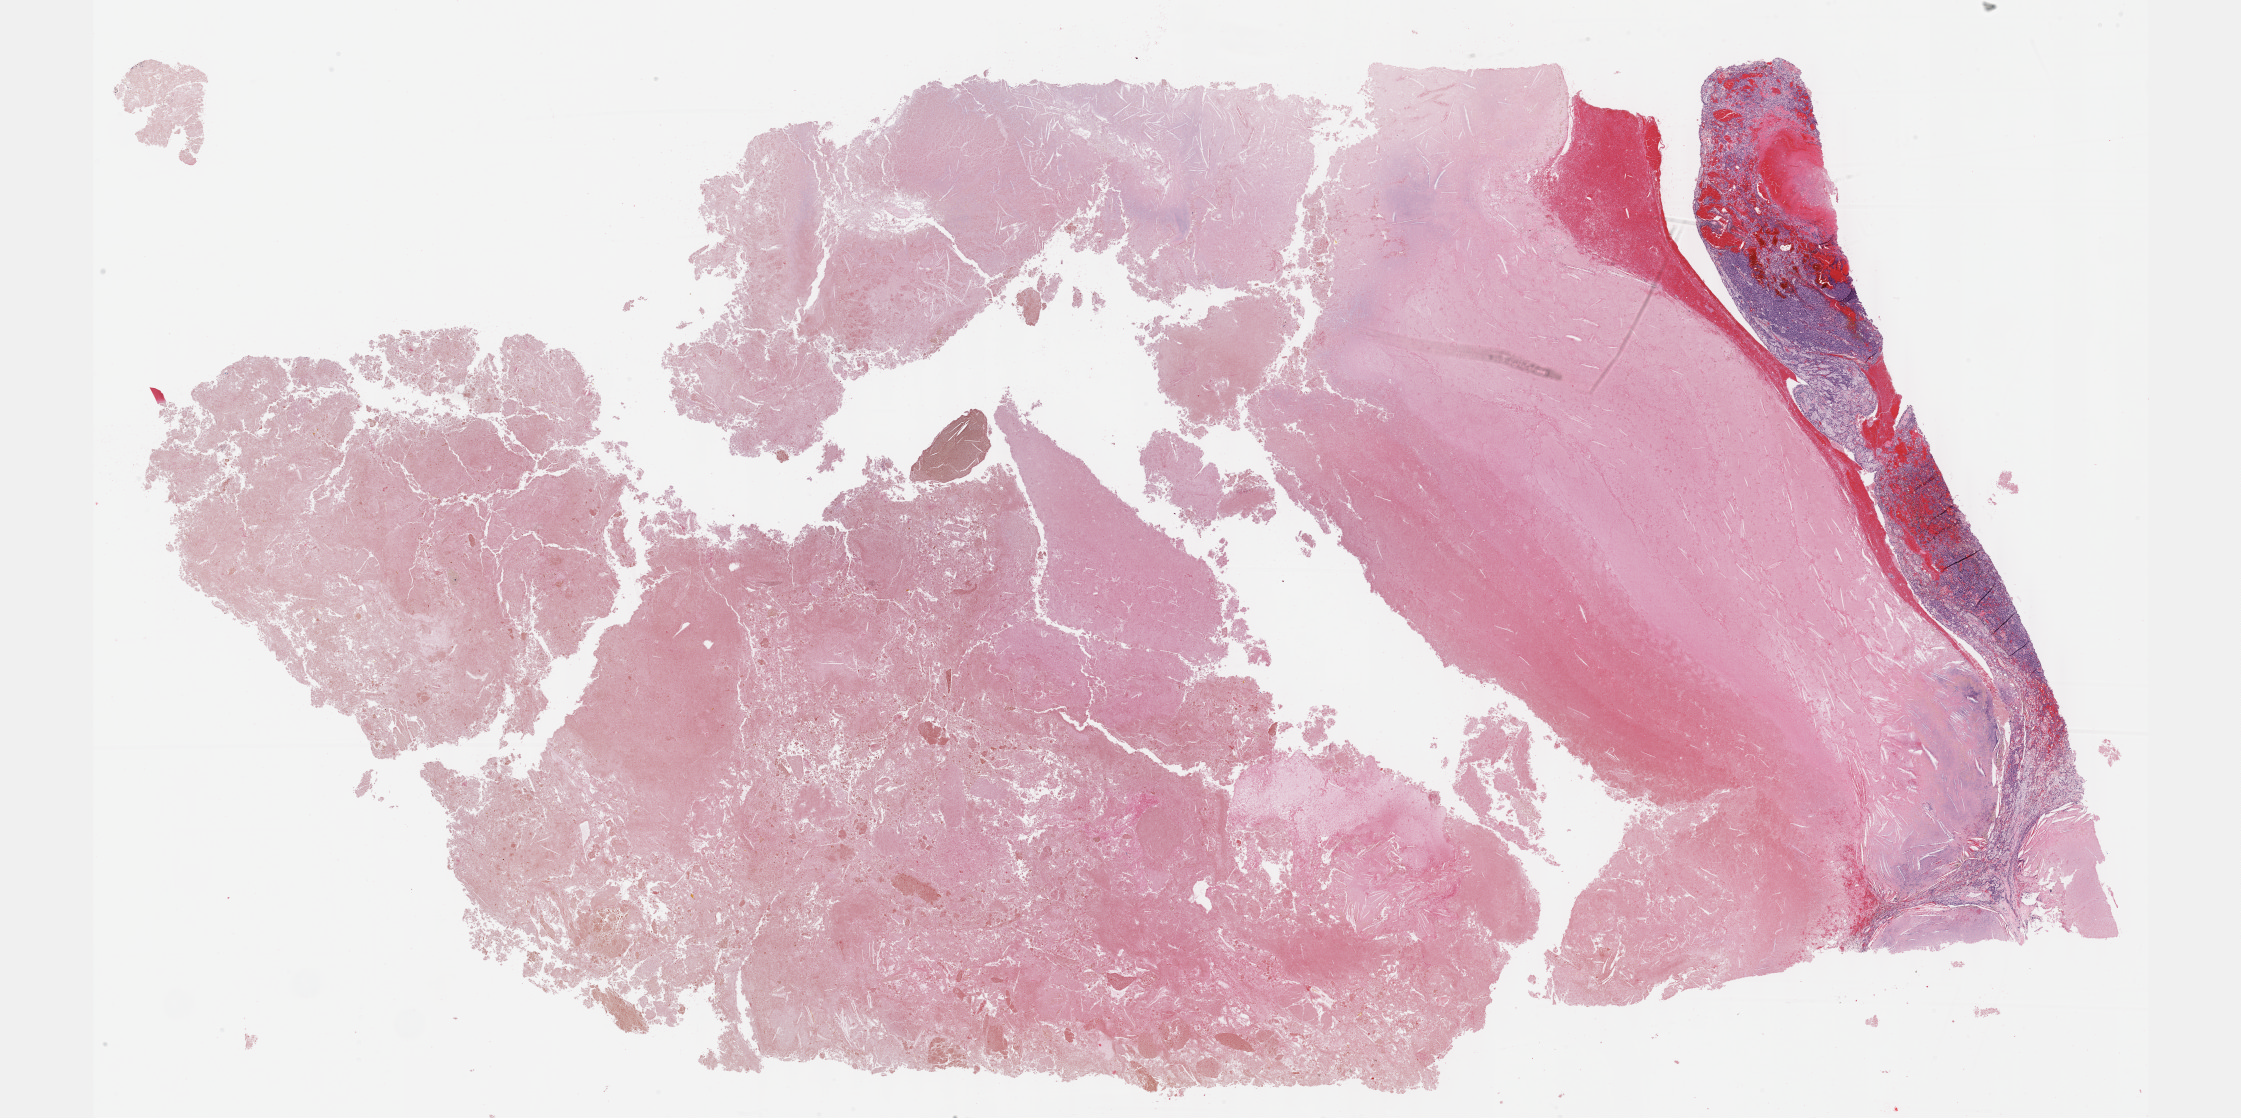
H&E whole-slide image — whole scanned area (about 36.2 x 18.1 mm, from a 40x scan) shown as a low-resolution overview. Formalin-fixed paraffin-embedded (FFPE) diagnostic section. Sample: primary tumour, kidney. Male, age 85 years at initial diagnosis.
- diagnosis: Papillary adenocarcinoma, NOS
- TNM: T1b NX M0
- AJCC pathologic stage: I (7th edition)